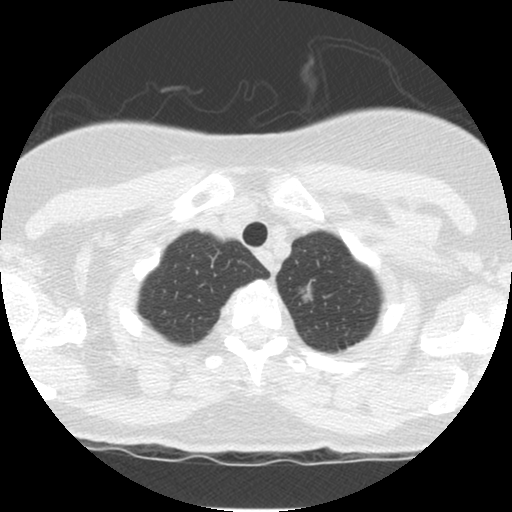
Low-dose screening chest CT, one axial slice; position 110 of 120 along the scan axis; lung window (W 1500 / L -600 HU); 512 × 512 image matrix.
Annotated regions visible in this slice (expert manual segmentation):
- lesion 1 (tumor, upper lobe of left lung): bounding box (x1, y1, x2, y2) in pixels: (299, 285, 314, 303)